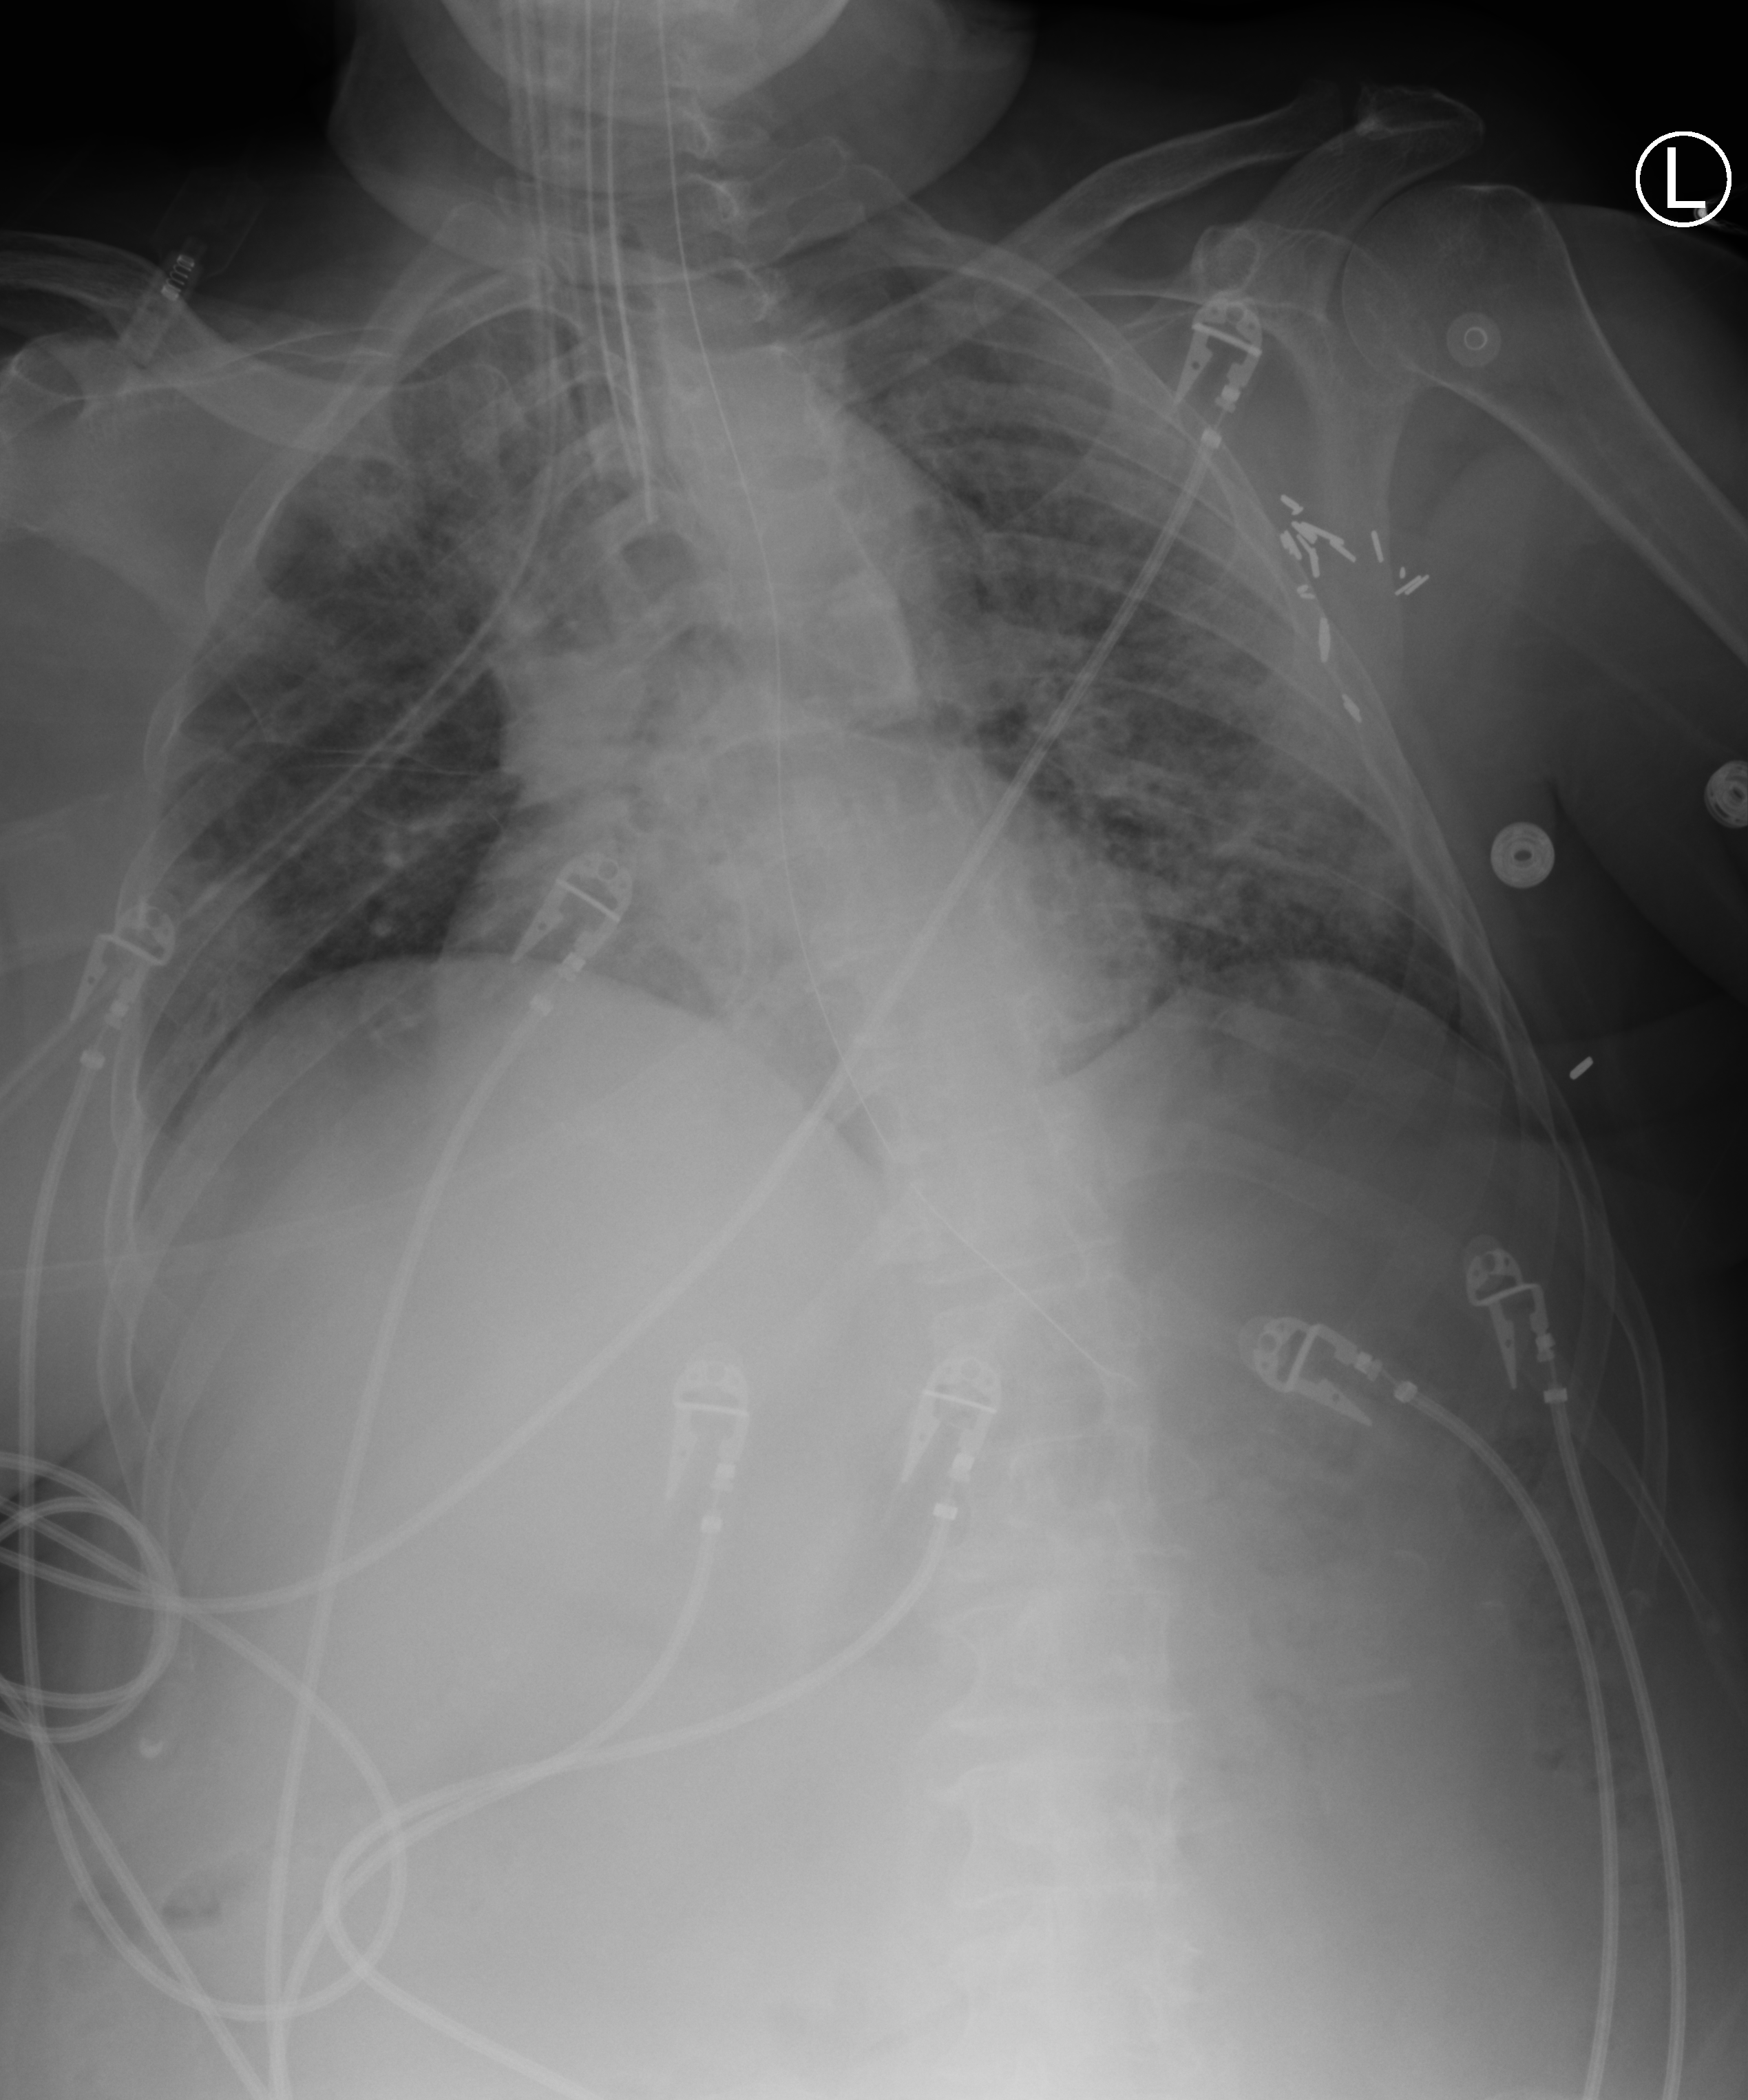
Chest X-ray (portable), anteroposterior (AP) projection. Female patient hospitalised with COVID-19, age 60–74 years.
From the hospital-stay record, not from the radiograph (when in the stay this image was taken is not recorded):
- mechanically ventilated during this hospital stay: yes
- admitted to intensive care during this hospital stay: yes
- hypertension (admission record): yes